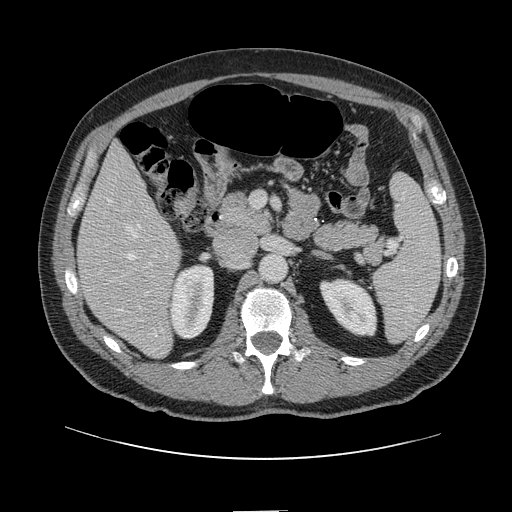
Contrast-enhanced abdominal CT, one axial slice; slice 56 of 161 in the series (ordered by position); 120 kVp; intravenous contrast given; soft-tissue window (W 400 / L 40 HU); 512 × 512 image matrix. Male patient, age 66 years. Case-level facts recorded for this patient, not image findings: diagnosis: colorectal cancer liver metastases, imaged before liver resection; multiple liver metastases: no; largest metastasis: 3.5 cm; disease in both lobes: no.
Annotated regions visible in this slice (manually delineated by an expert):
- hepatic veins: box from (x=110, y=201) to (x=157, y=336) px
- liver: (x=78, y=144)–(x=180, y=357)
- planned liver remnant (the part of the liver to remain after resection): (x=78, y=145)–(x=167, y=280)
- portal vein (with intrahepatic branches): (x=143, y=249)–(x=159, y=297)